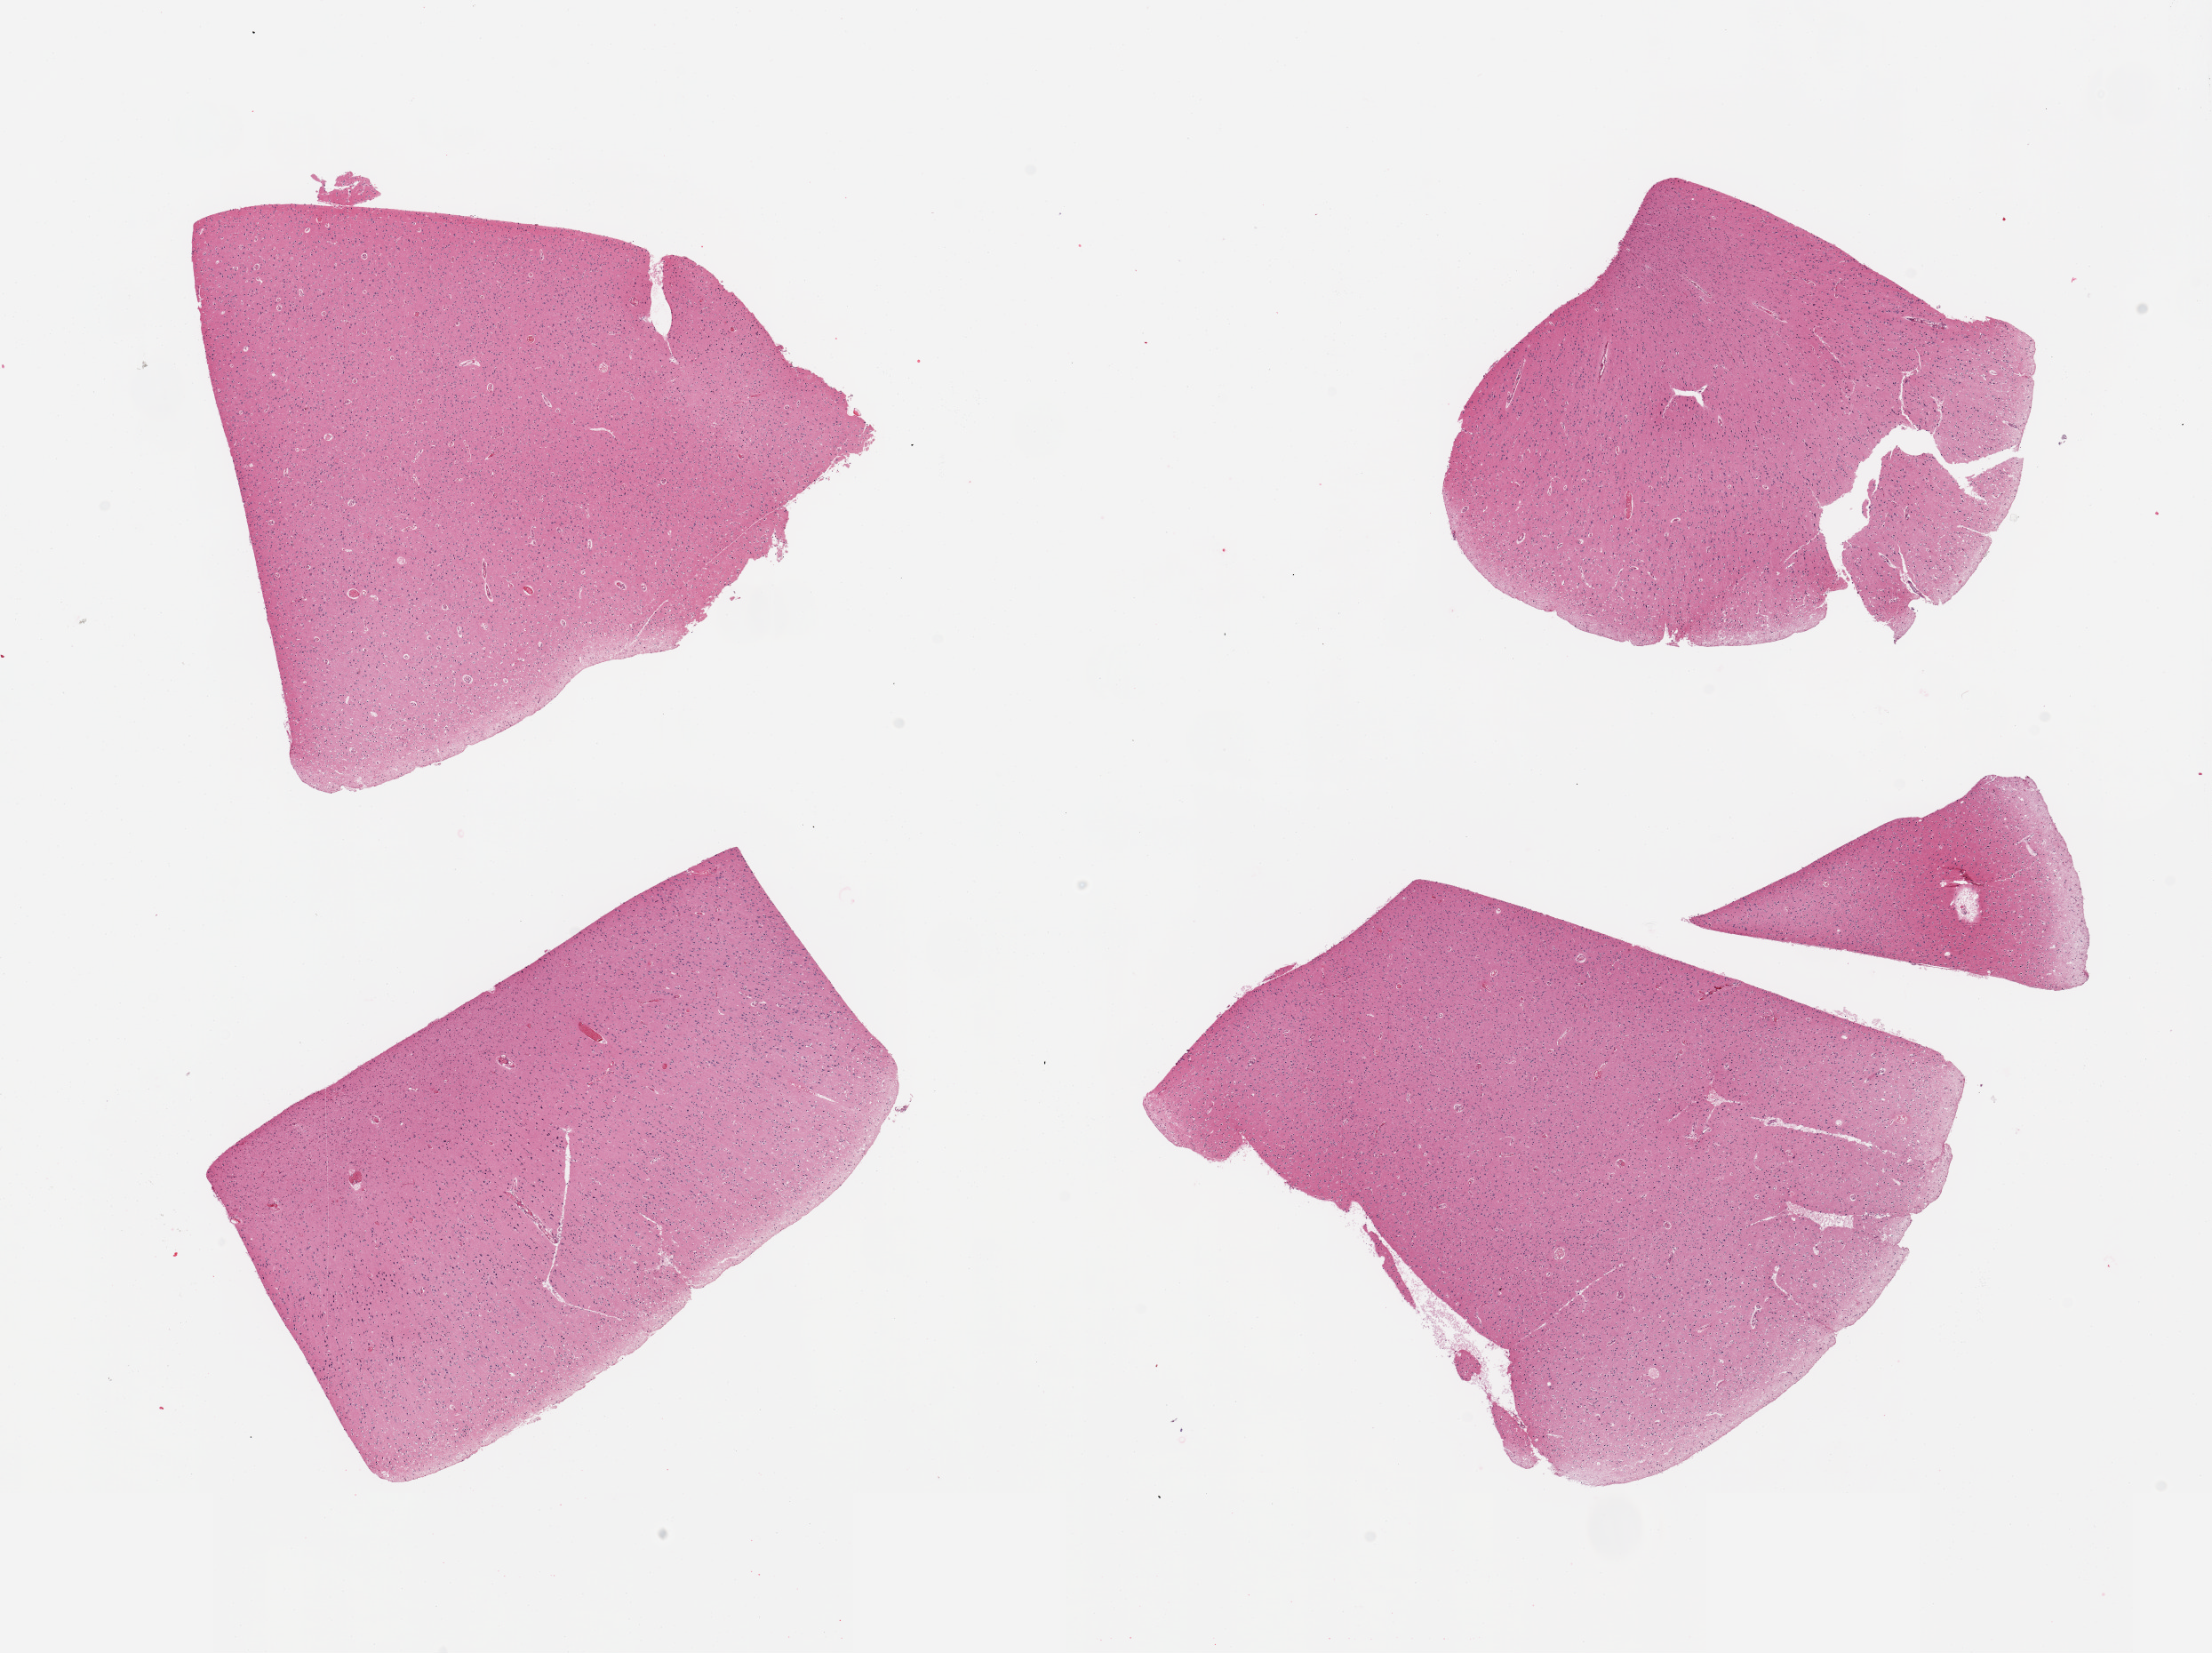
Whole-slide image, H&E stain, a low-resolution overview of the entire scanned area, about 19.7 x 14.7 mm. PAXgene-fixed, paraffin-embedded tissue. Sampled site (target tissue): cerebral cortex. Donor tissue sample. Donor sex: female.
Reviewer comment on this tissue sample: 4 pieces; mild to moderate autolysis.